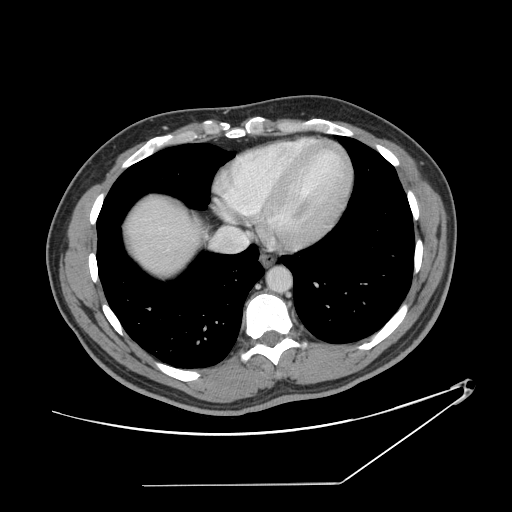
Contrast-enhanced abdominal CT, one axial slice. Slice 138 of 152 in the series (ordered by position). Reconstruction kernel STANDARD. 120 kVp. Intravenous contrast given. Soft-tissue window (W 400 / L 40 HU). 2.5 mm slice thickness. 512 × 512 image matrix, field of view 432 × 432 mm. Male patient, age 45 years. From the clinical record (not read from this slice): diagnosis: colorectal cancer liver metastases, imaged before liver resection; multiple liver metastases: no; largest metastasis: 1 cm; disease in both lobes: no.
Annotated regions visible in this slice (manually delineated by an expert):
- hepatic veins: bounding box [x1, y1, x2, y2] px = [228, 228, 248, 245]
- liver: [128, 196, 197, 276]
- planned liver remnant (the part of the liver to remain after resection): [128, 196, 197, 276]